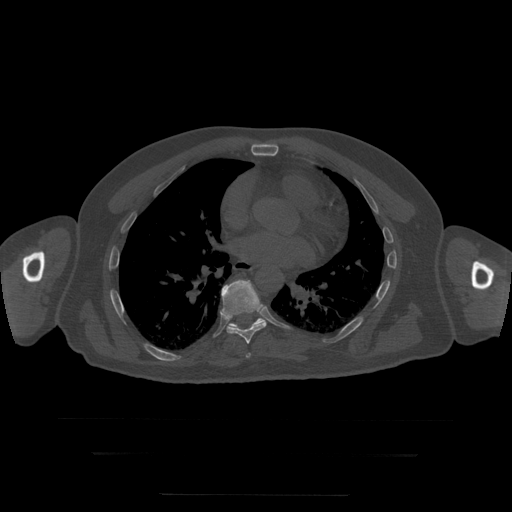
CT including the spine, one axial slice. Slice 161 of 397 in the series (ordered by position). 120 kVp. Bone window (W 1800 / L 400 HU). 1.25 mm slice thickness. 512 × 512 image matrix, field of view 510 × 510 mm. Patient age 73 years. Case-level facts recorded for this patient, not image findings: primary cancer: prostate.
Structures marked on this image (semi-automatic segmentation, software-assisted and operator-edited):
- T7 vertebra: box from (x=246, y=353) to (x=251, y=358) px
- T8 vertebra: (x=221, y=280)–(x=267, y=344)
- T9 vertebra: (x=229, y=318)–(x=265, y=330)